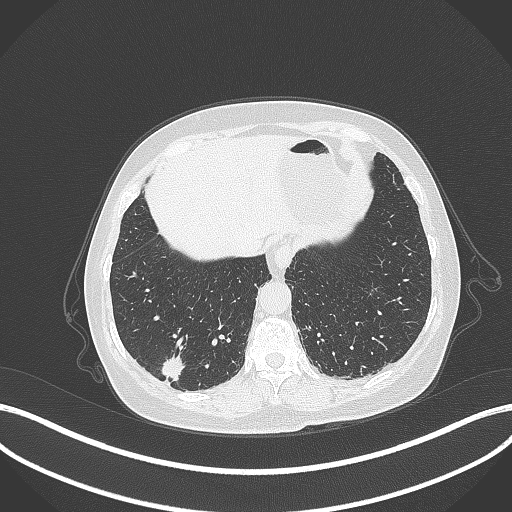
Chest CT, one axial slice; slice 59 of 333 in the series (ordered by position); 120 kVp; lung window (W 1500 / L -600 HU); 512 × 512 image matrix, field of view 400 × 400 mm. Patient: female, 69 years. From the clinical record (not read from this slice): clinical TNM (as recorded): T1b N0 M0; histopathological grade: G2-3.
Structures marked on this image (bounding box drawn by a radiologist):
- lung tumour (recorded histology: adenocarcinoma): bounding box (x1, y1, x2, y2) in pixels: (157, 348, 187, 383)